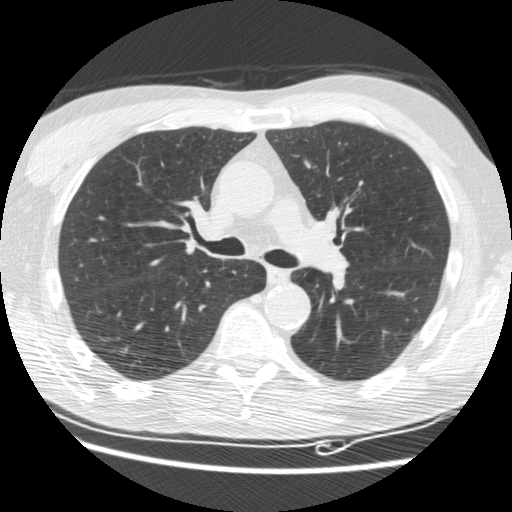
Axial slice from a low-dose chest CT screening exam; third screening round (two years after baseline); lung window (W 1500 / L -600 HU); 2.5 mm slice thickness; standard (soft-tissue) reconstruction kernel (STANDARD); slice 70 of 176 in the series; 512 × 512 image matrix, field of view 347 × 347 mm. Male, age 62 years at enrolment. Current smoker at enrolment.
Expert reader's lesion annotation, bounding box [x1, y1, x2, y2] px = [97, 331, 146, 374]. The screening reader recorded 3 non-calcified nodules or masses ≥4 mm on this exam; which of them this box marks is not recorded. Official screen result: positive, other.